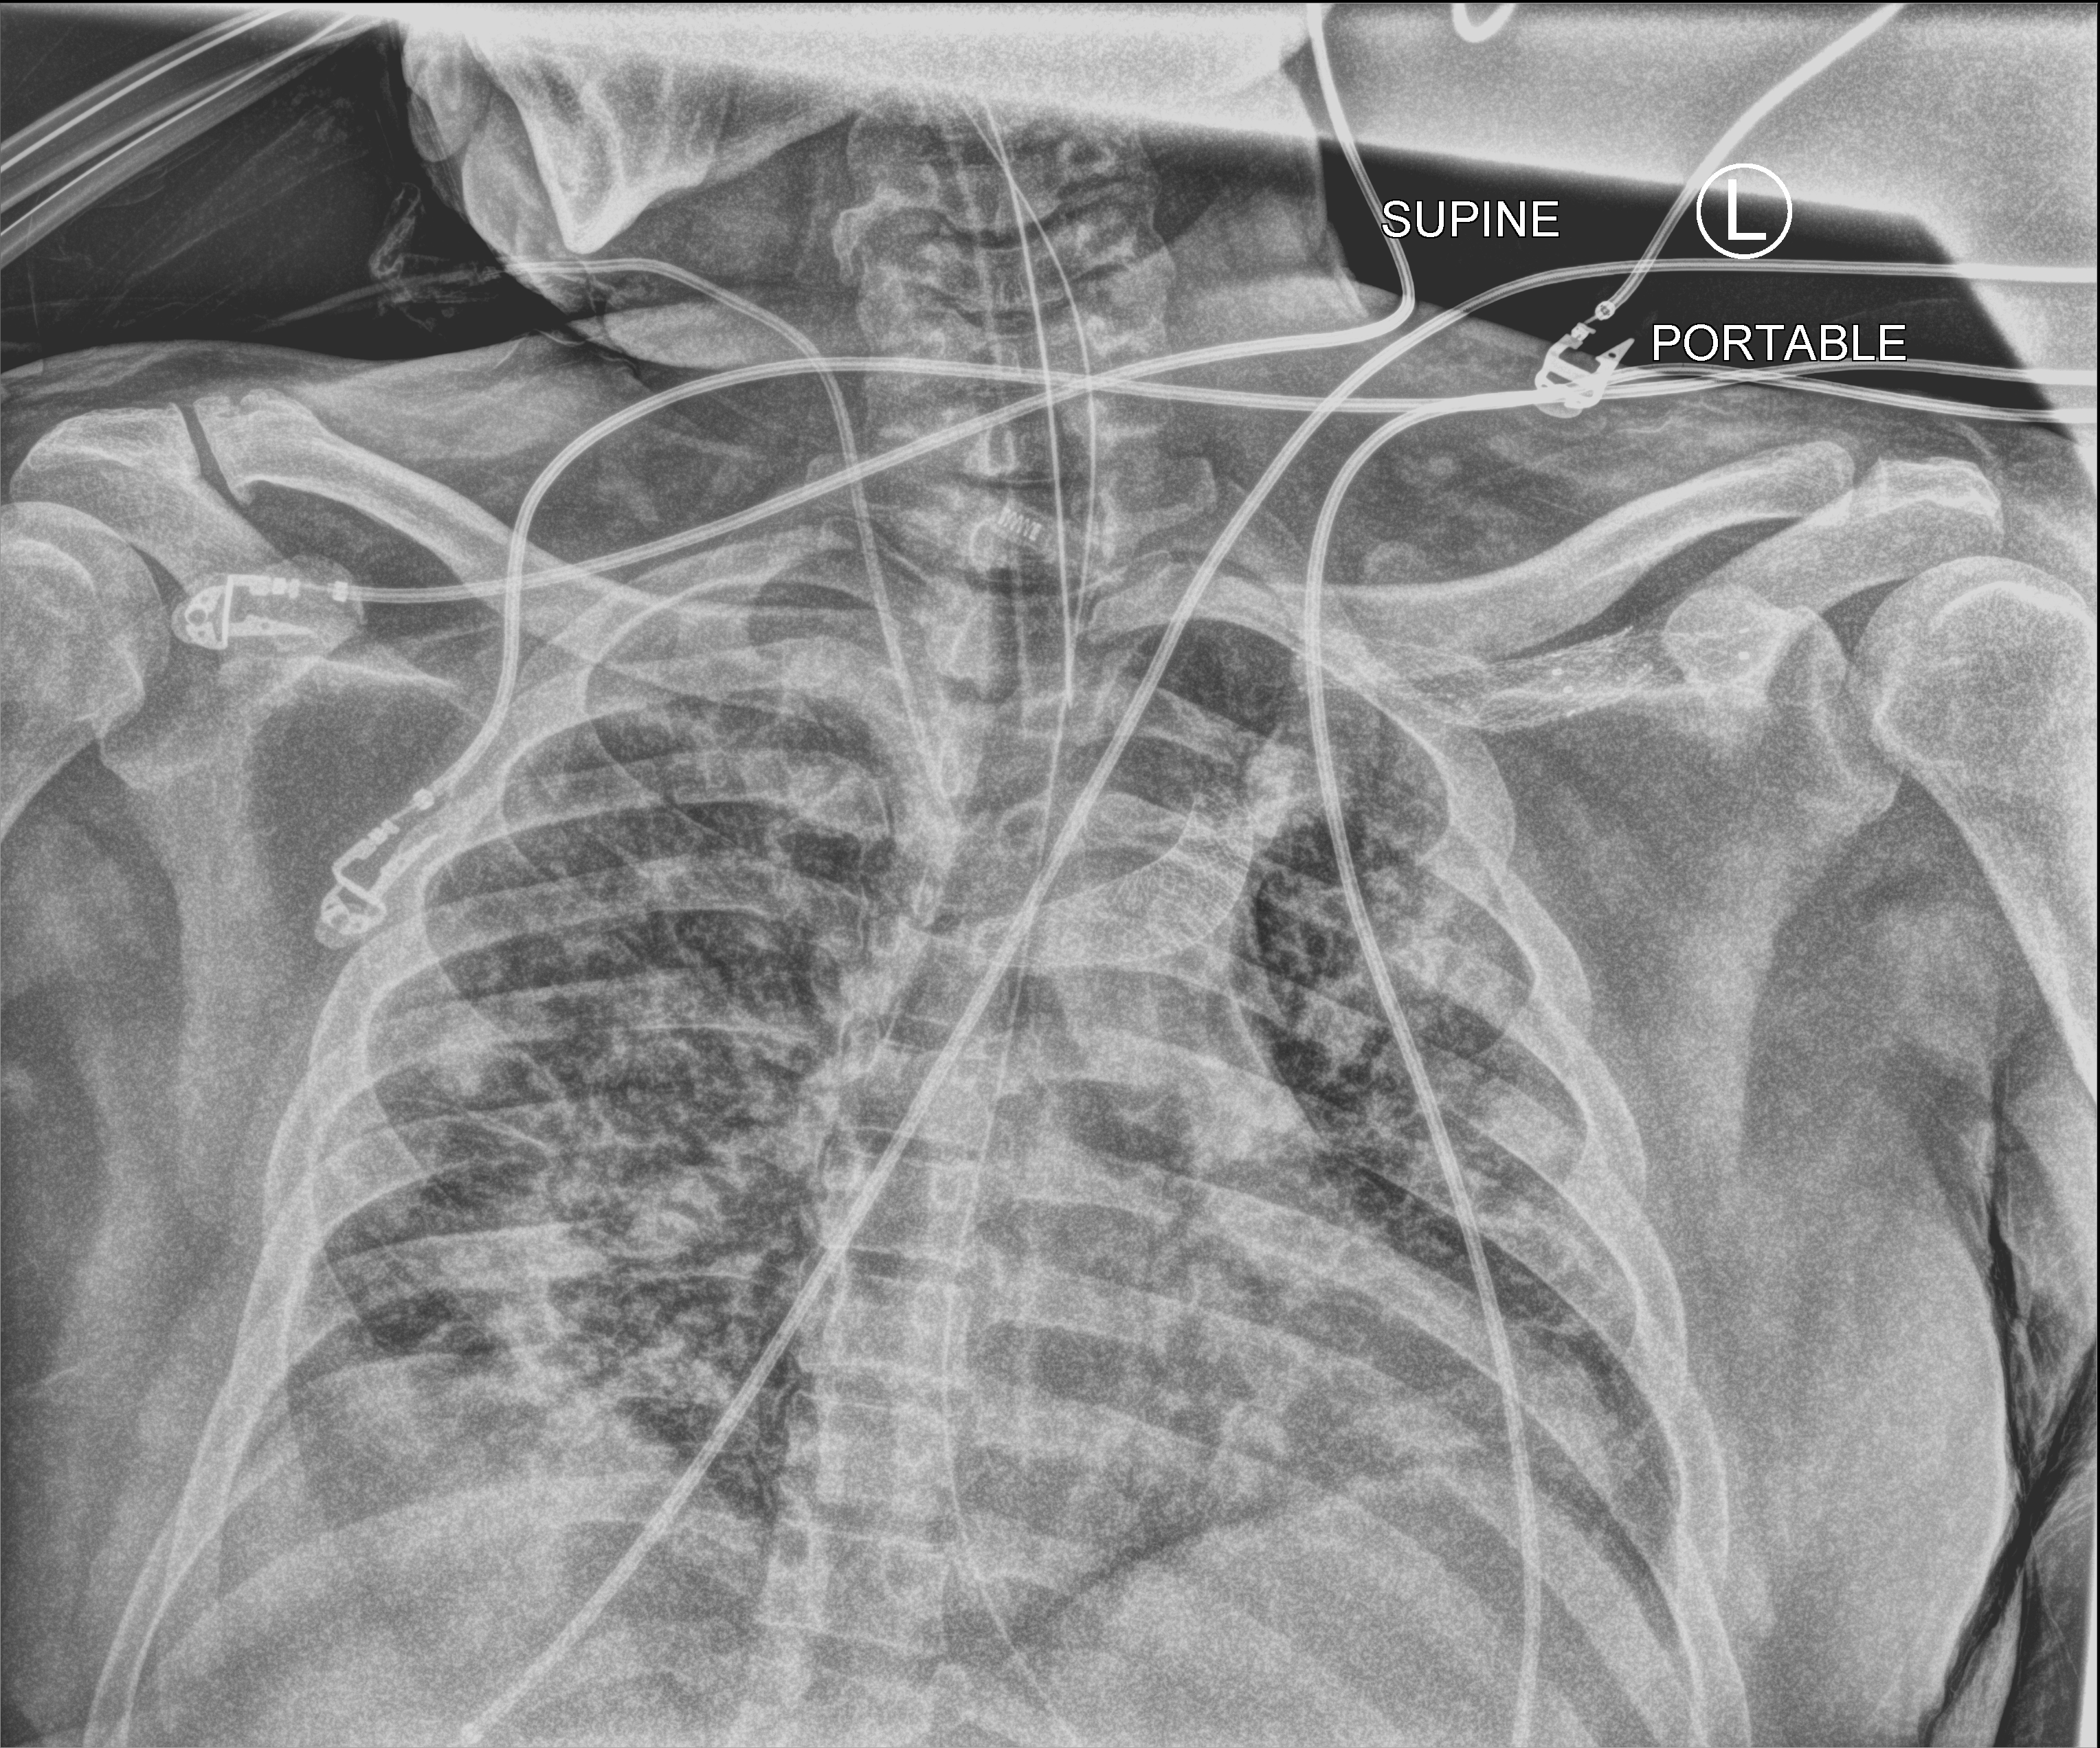
Chest X-ray (portable), anteroposterior (AP) projection. Male patient hospitalised with COVID-19, age 18–59 years.
Hospital-stay facts (about this admission, not read from this image; timing relative to this image not recorded): length of hospital stay: 41 days.